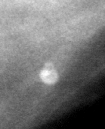
Cropped region of a digitized screen-film mammogram centred on a radiologist-marked abnormality; left breast; MLO view; BI-RADS breast density category 3 (scale 1–4).
- Calcifications, morphology round and regular / lucent centered; BI-RADS assessment category 2; benign without callback (not worked up further).